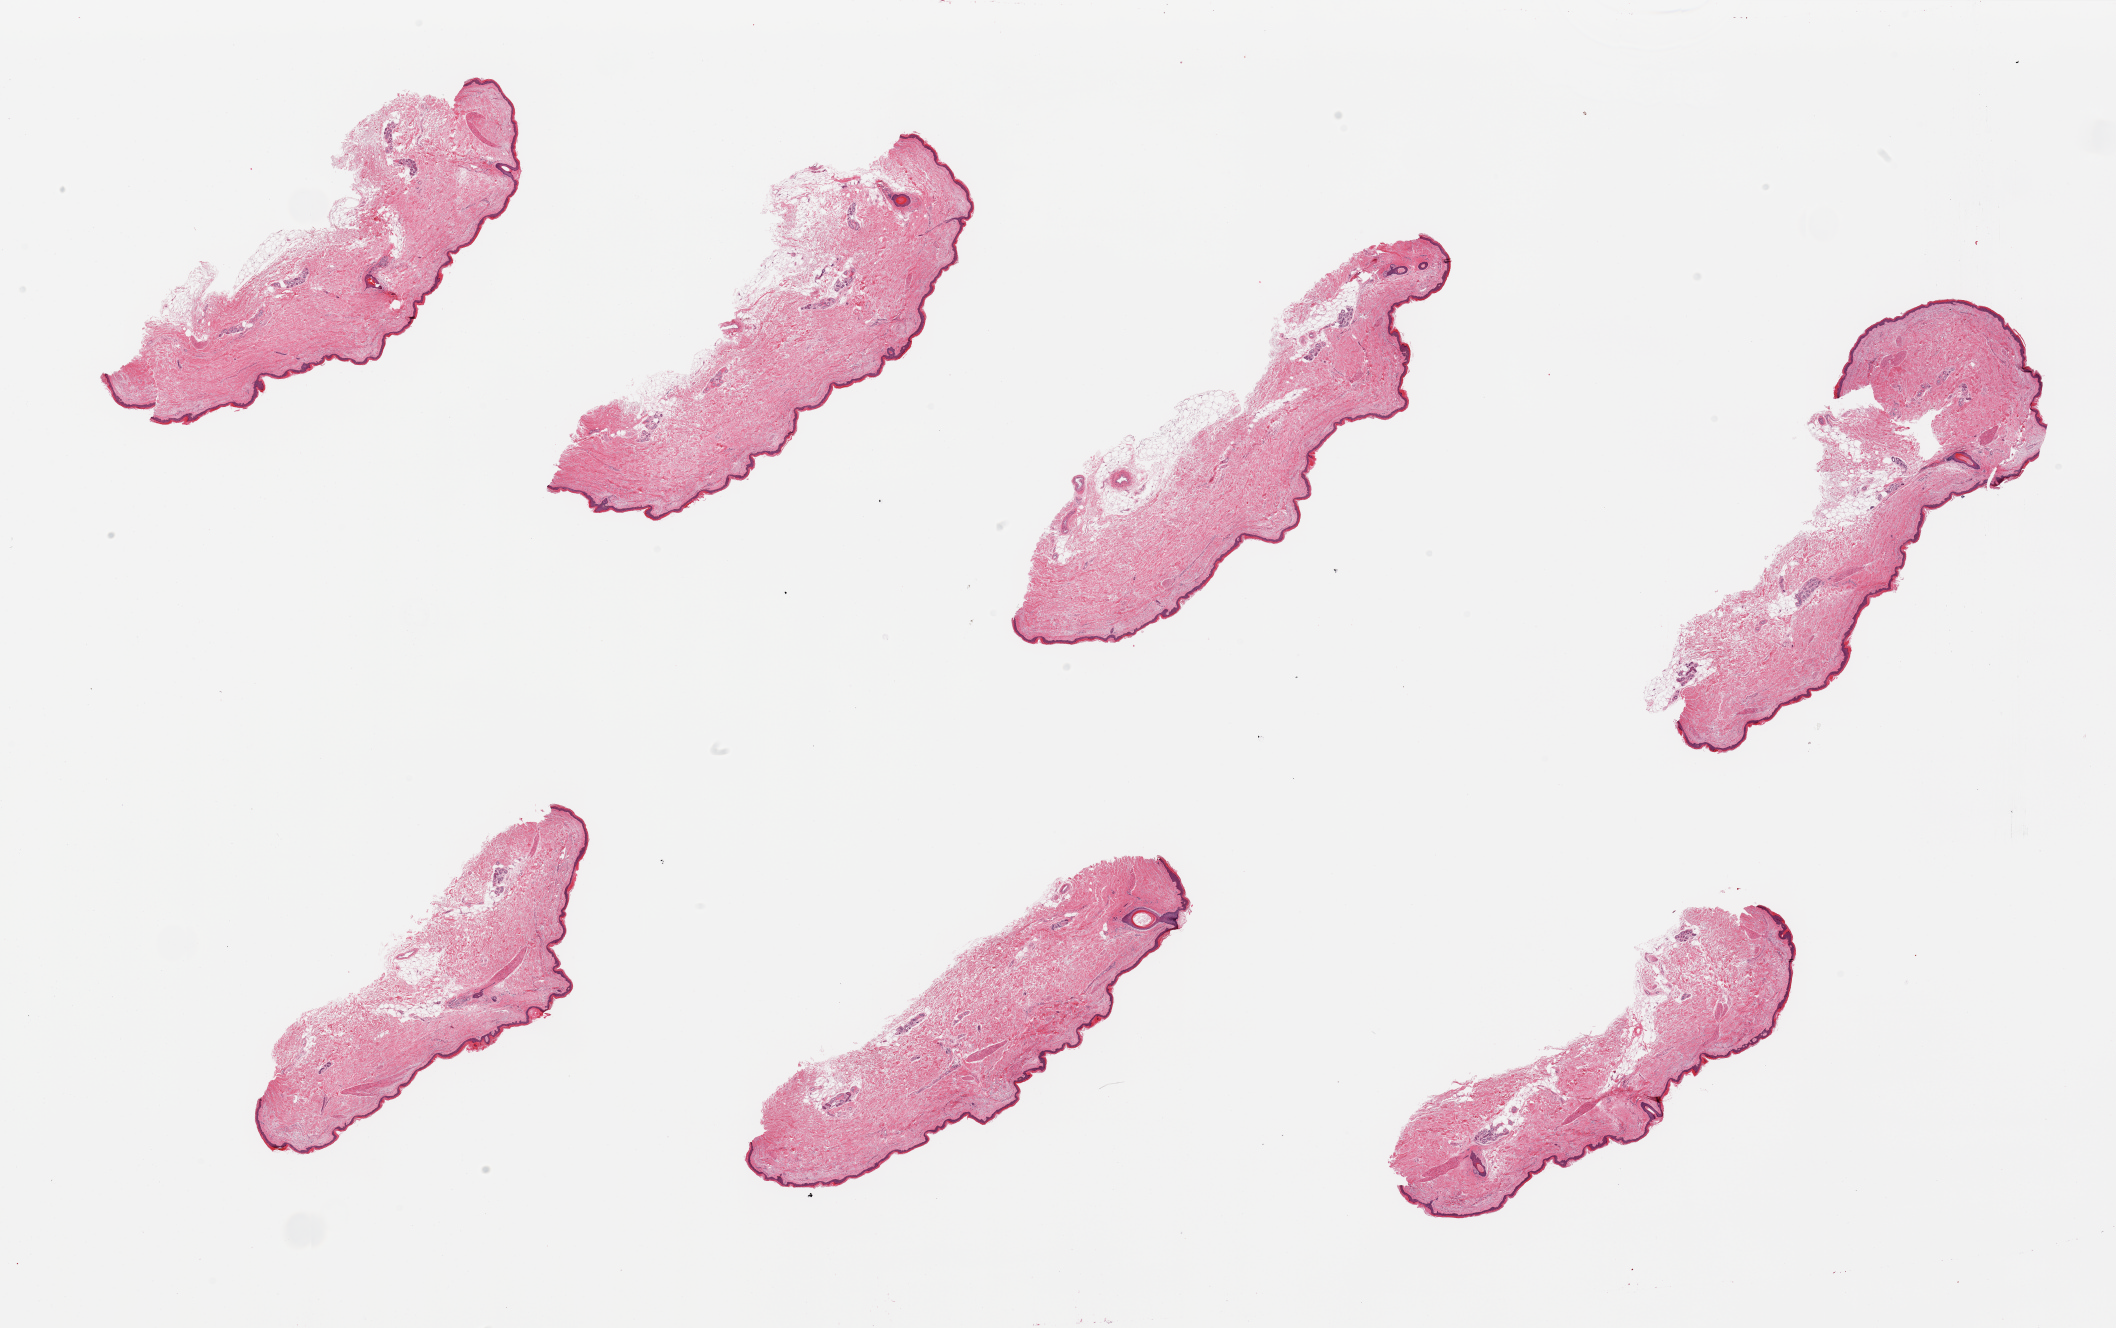
Whole-slide image, haematoxylin and eosin stain — shown as a low-resolution overview of the whole scanned area (about 33.5 x 21.0 mm, acquisition: 20x scan), PAXgene-fixed paraffin-embedded (PFPE) section, target tissue: skin of lower leg, tissue donor sample. Donor: male.
* reviewer comment on this tissue sample: 7 pieces; subcutaneous fat on 3; up to 20% intradermal fat